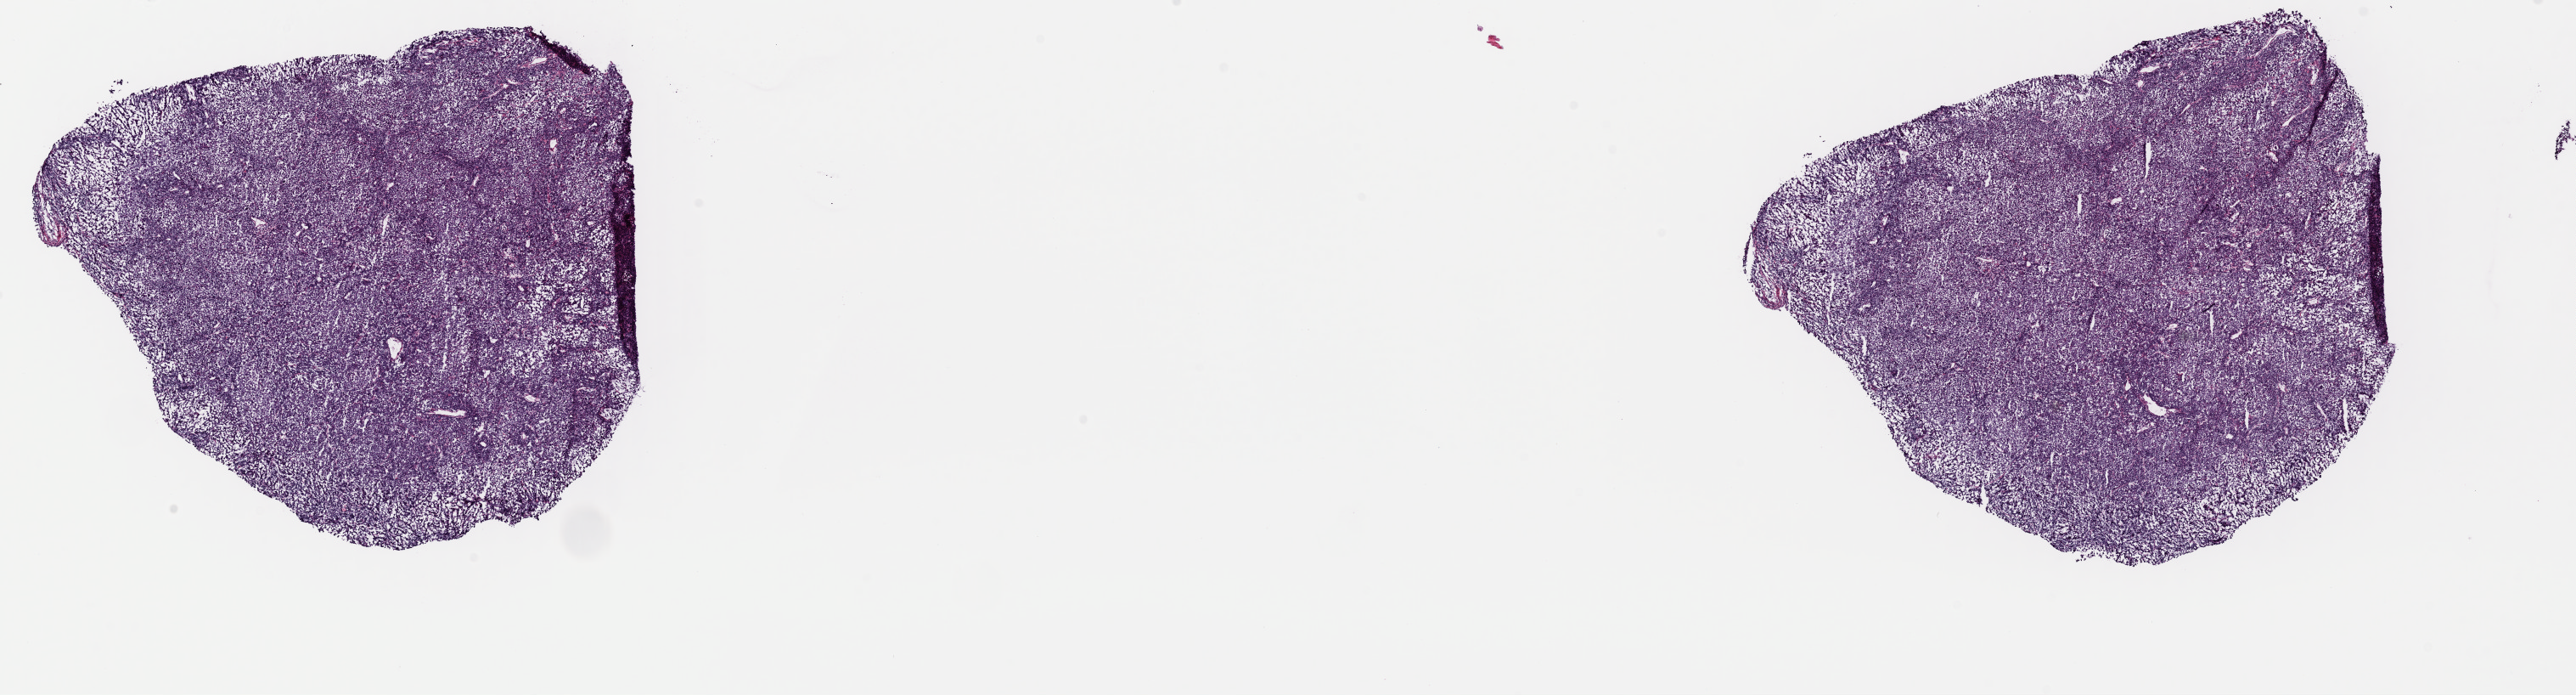
Digitized H&E tissue section (whole slide), a low-resolution overview of the entire scanned area, about 24.0 x 6.5 mm (from a 40x scan). Frozen section from the top of the tissue portion. Metastatic tumour sample, sampled site: lymph node. Patient: male, age at initial diagnosis 65 years. Composition of this section per pathologist review: tumour cells 100%, tumour nuclei 95%, normal cells 0%, stromal cells 0%, necrosis 0%. Infiltration values recorded for this section: lymphocyte infiltration 0%, monocyte infiltration 0%, neutrophil infiltration 0%.
This section: metastatic tumour tissue. Patient diagnosis: Malignant melanoma, NOS.